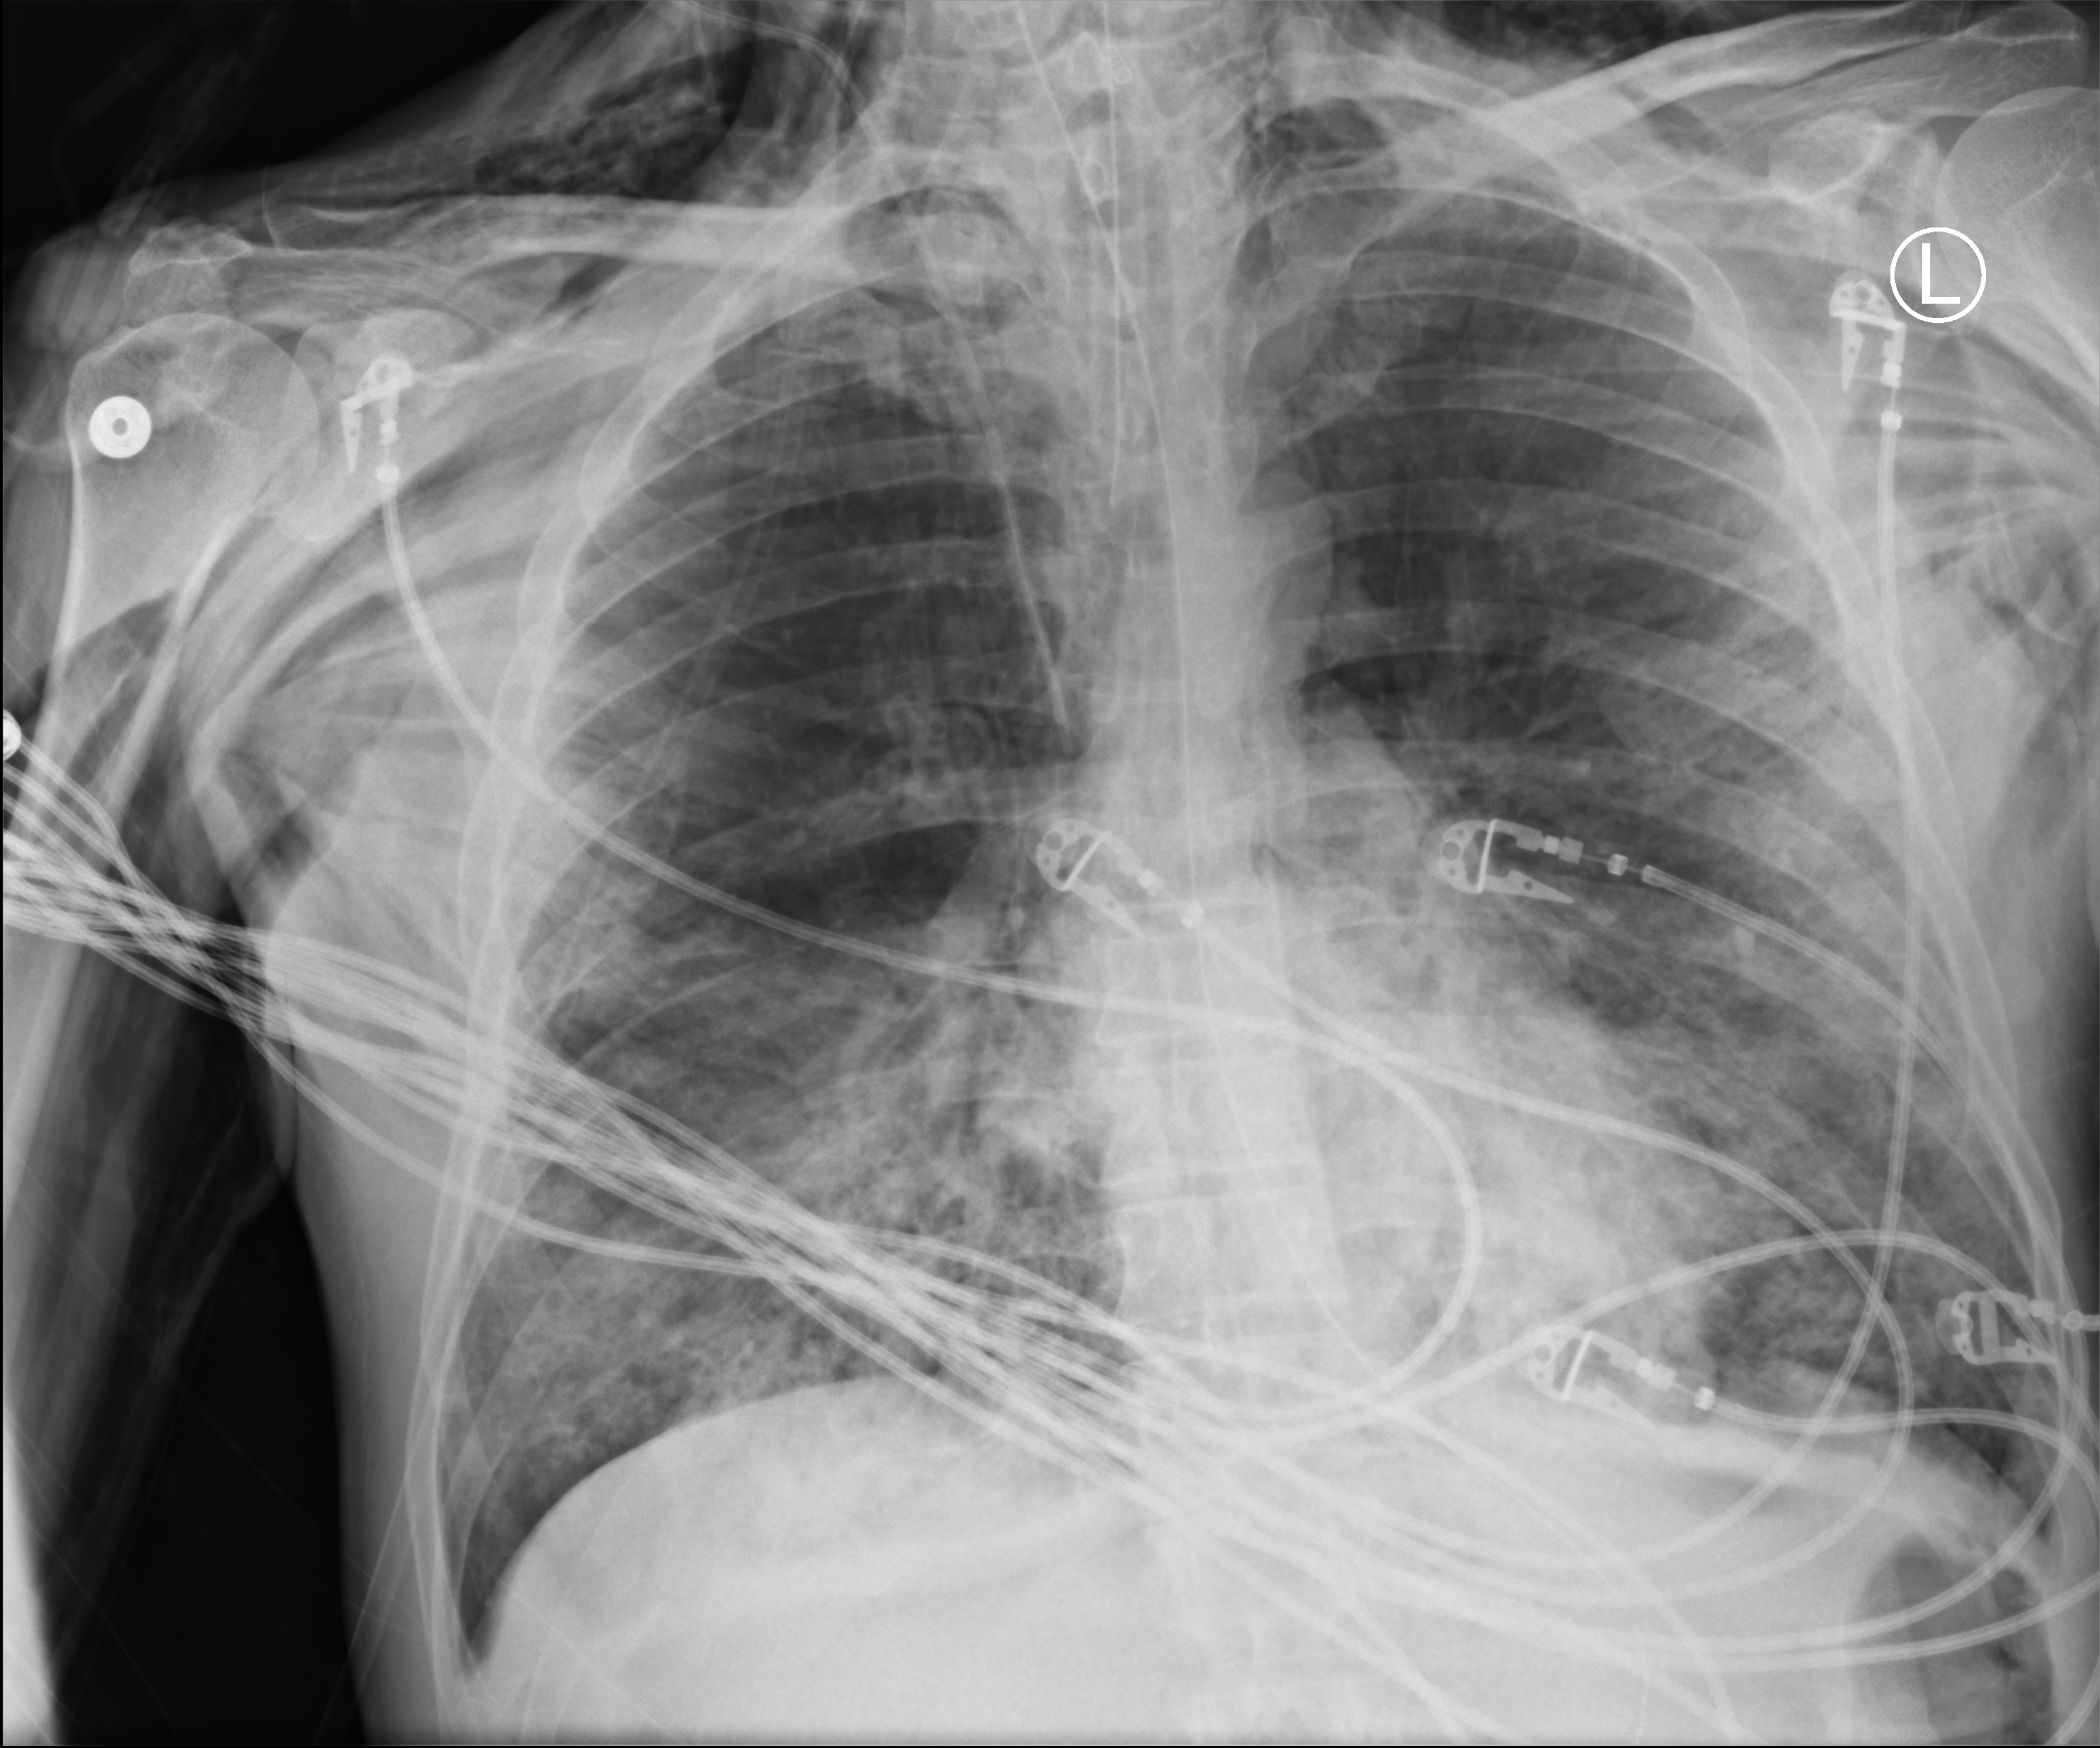
Bedside chest radiograph (computed radiography); anteroposterior (AP) projection. Male patient hospitalised with COVID-19, age 18–59 years.
From the hospital-stay record, not from the radiograph (when in the stay this image was taken is not recorded):
- admitted to intensive care during this hospital stay: yes